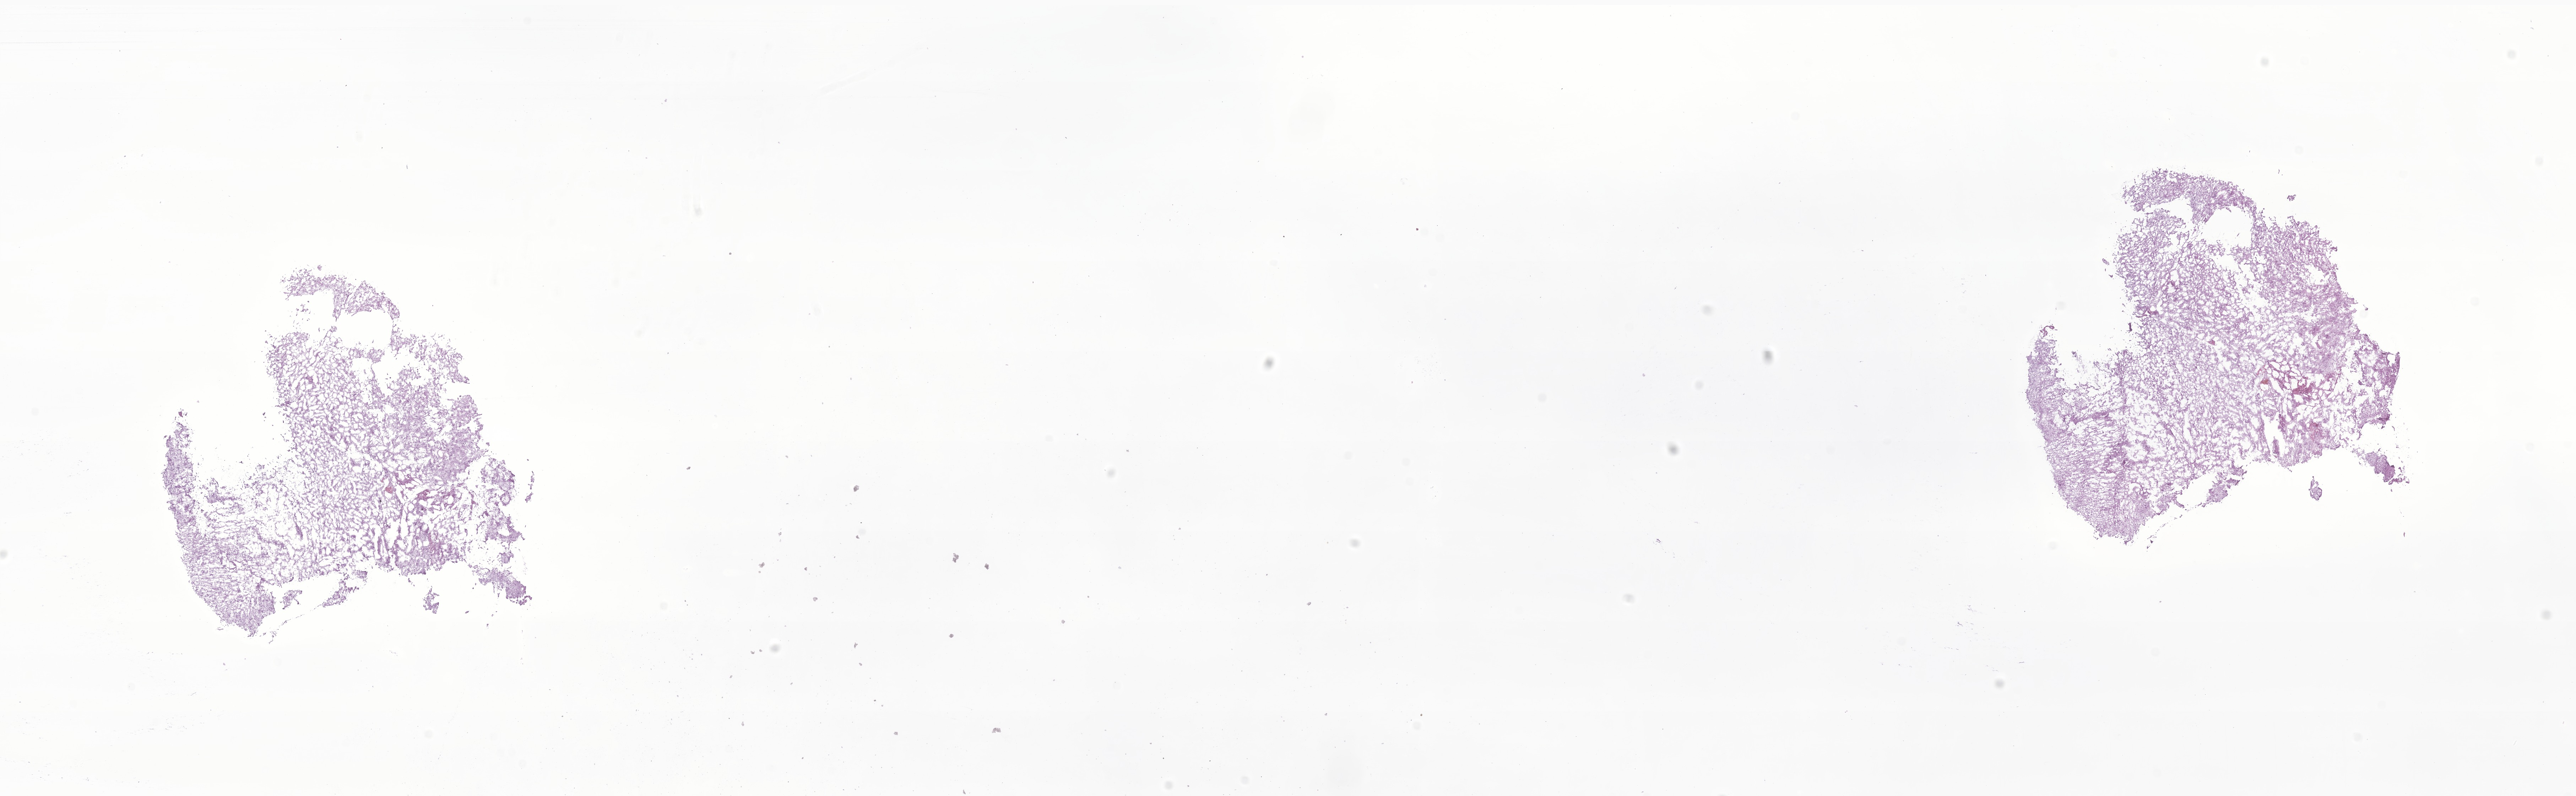
Whole-slide image, haematoxylin and eosin stain of tumor tissue from the brain — low-resolution overview of the scanned area, about 30.6 x 9.4 mm, cryosection (OCT / tissue freezing medium). Patient: male, age 149 months (12 years 5 months).
Diagnosis (ICD-O-3 morphology term): Glioma, malignant.